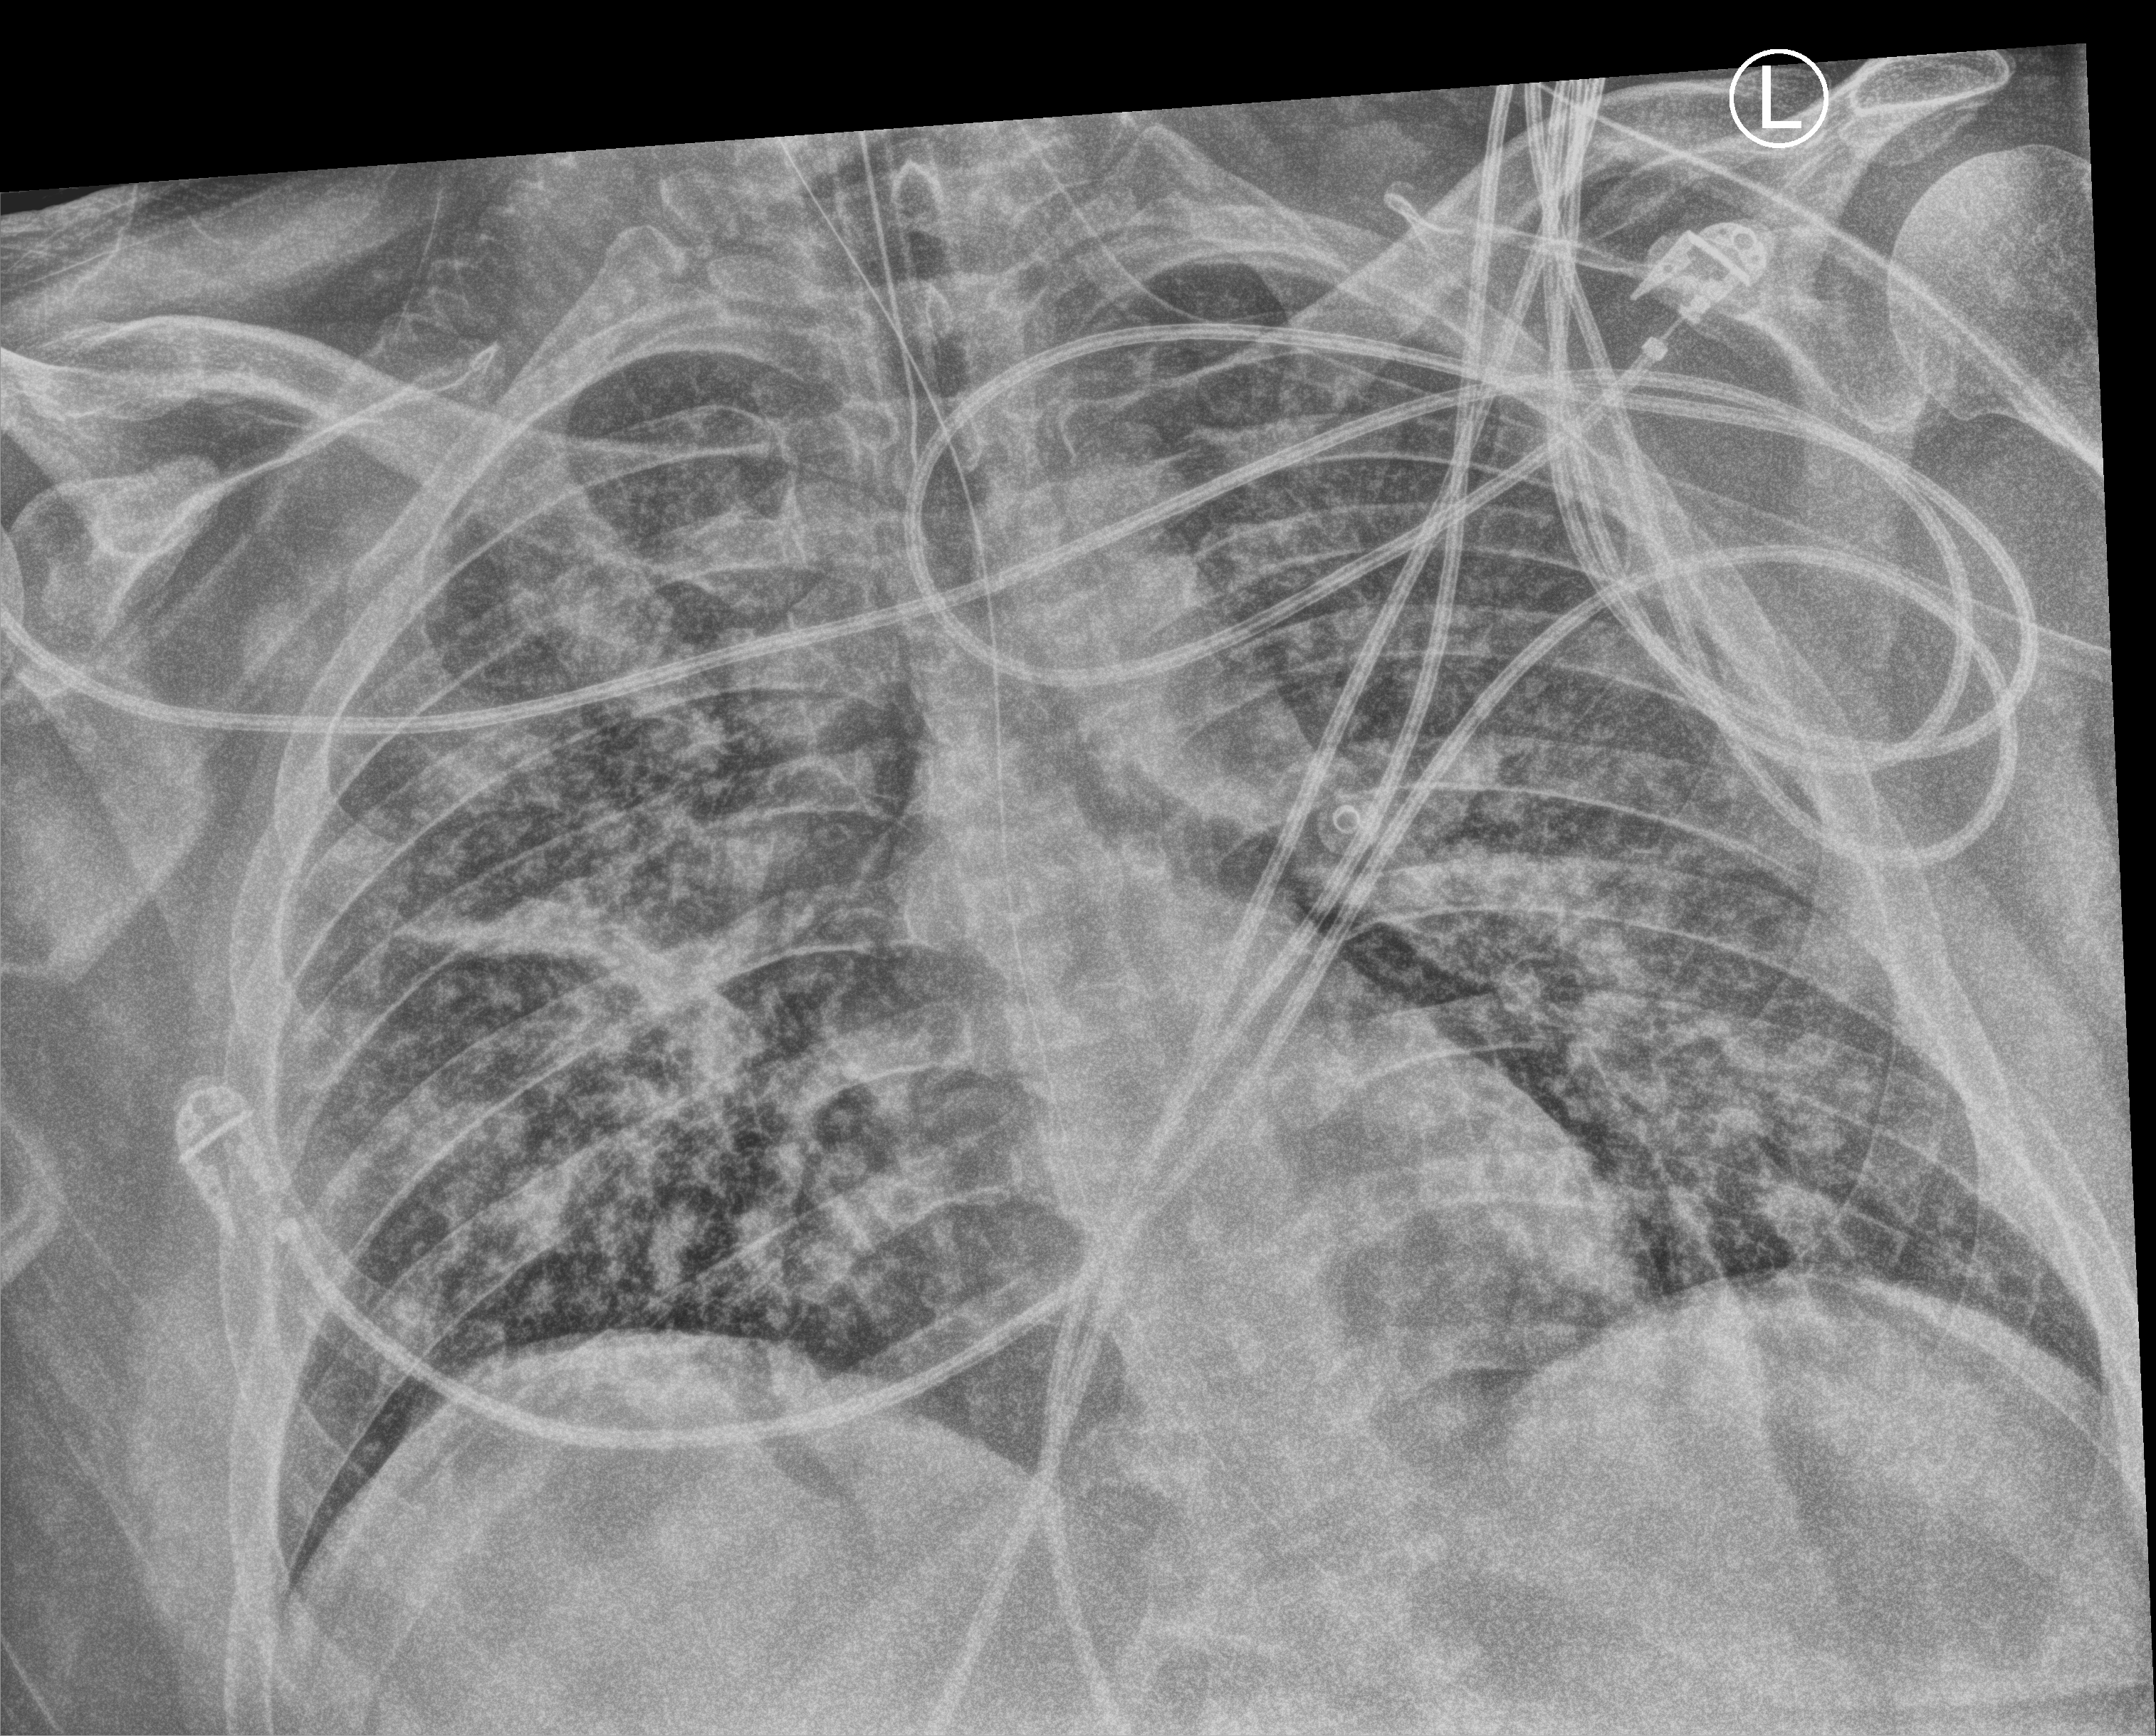
Chest X-ray (portable); anteroposterior (AP) projection. Patient hospitalised with COVID-19, aged 18–59 years.
From the hospital-stay record, not from the radiograph (when in the stay this image was taken is not recorded): mechanically ventilated during this hospital stay: yes; length of hospital stay: 31 days.